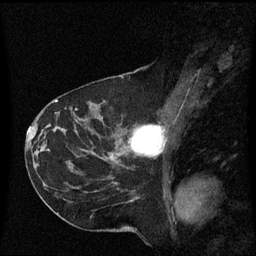
Breast MRI (dynamic contrast-enhanced), one sagittal slice. Slice 33 of 60 in the series (ordered by position). Dynamic contrast-enhanced series, image 2 of 3 at this slice position (ordered by acquisition). 1.5 T. TE 4.2 ms, TR 8.4 ms. 2 mm slice thickness. 256 × 256 image matrix, field of view 220 × 220 mm. Female patient, age 41 years. From the clinical record (not read from this slice): setting: breast cancer imaged before/during neoadjuvant chemotherapy; receptor status: triple-negative.
Outlined on this slice (semi-automatic segmentation, software-assisted and operator-edited):
- analysis volume of interest (the breast-tissue region the enhancement analysis was run in; not a lesion): bounding box [x1, y1, x2, y2] px = [116, 108, 167, 163]
- tumour enhancement mask (voxels above the 70 % enhancement threshold inside the analysis volume of interest): [129, 126, 164, 157]